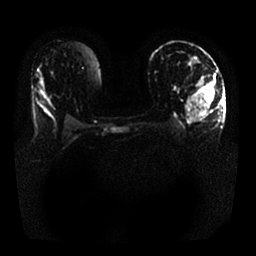
Breast MRI, one axial slice. Position 15 of 25 along the scan axis. Diffusion-weighted series; image 2 of 4 stored at this slice position (different b-values; order by instance number). 1.5 T. 4 mm slice thickness. 256 × 256 image matrix. Female patient.
Structures marked on this image (outlined manually by an expert reader):
- tumour on diffusion-weighted imaging: bounding box <190,81,214,122> (left, top, right, bottom; pixels)